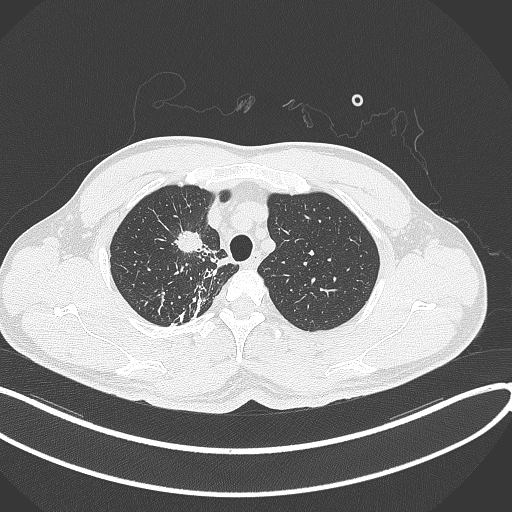
Chest CT, one axial slice; reconstruction kernel B70f; lung window (W 1500 / L -600 HU); 512 × 512 image matrix, field of view 400 × 400 mm. Patient: male, 48 years. Case-level facts recorded for this patient, not image findings: clinical TNM (as recorded): T1c N1 M1.
Annotated regions visible in this slice (bounding box drawn by a radiologist):
- lung tumour (recorded histology: adenocarcinoma): box from (x=169, y=225) to (x=209, y=263) px